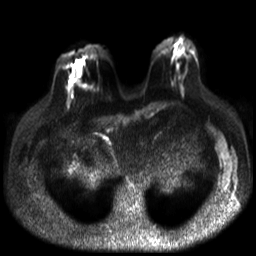
Breast MRI, one axial slice. Diffusion-weighted series; image 2 of 4 stored at this slice position (different b-values; order by instance number). 3 T. 4 mm slice thickness. 256 × 256 image matrix. Female patient.
Structures marked on this image (manually delineated by an expert):
- tumour on diffusion-weighted imaging: bounding box (x1, y1, x2, y2) in pixels: (69, 72, 80, 89)